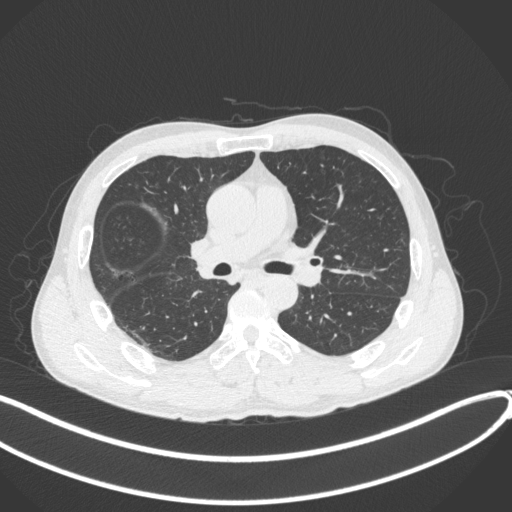
Chest CT, one axial slice. Position 225 of 409 along the scan axis. Reconstruction kernel B31f. 120 kVp. Lung window (W 1500 / L -600 HU). 512 × 512 image matrix, field of view 400 × 400 mm. Patient: male, 53 years. Case-level facts recorded for this patient, not image findings: clinical TNM (as recorded): T1b N0 M0.
Outlined on this slice (rectangle marked by the reading radiologist):
- lung tumour (recorded histology: squamous cell carcinoma): bounding box [x1, y1, x2, y2] px = [187, 234, 223, 282]